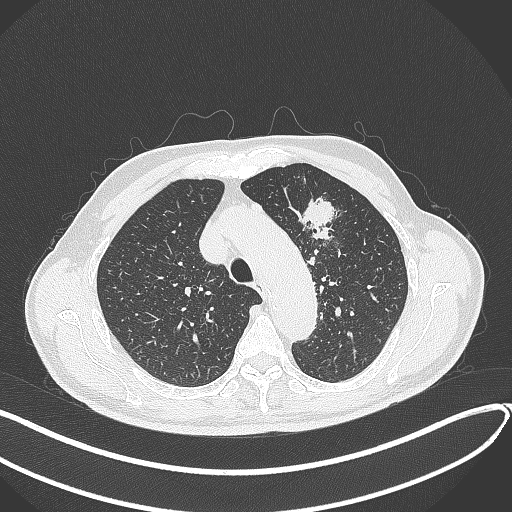
Chest CT, one axial slice. Slice 315 of 459 in the series (ordered by position). Lung window (W 1500 / L -600 HU). 512 × 512 image matrix, field of view 400 × 400 mm. Patient: male, 74 years. Case-level facts recorded for this patient, not image findings: clinical TNM (as recorded): T2b N0 M1c.
Outlined on this slice (bounding box drawn by a radiologist):
- lung tumour (recorded histology: adenocarcinoma): bounding box (x1, y1, x2, y2) in pixels: (295, 193, 339, 246)